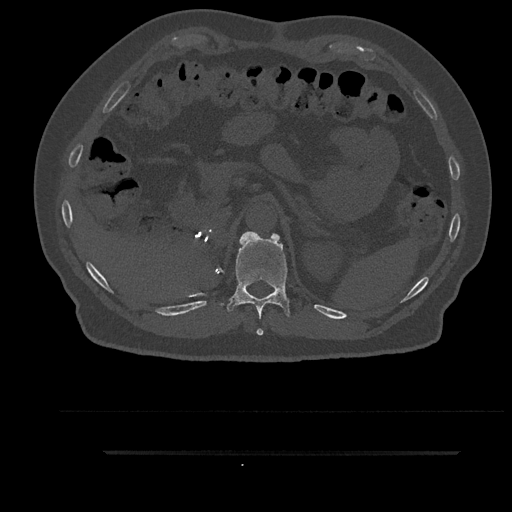
CT including the spine, one axial slice. Reconstruction kernel Br40s/3. 120 kVp. Bone window (W 1800 / L 400 HU). 0.5 mm slice thickness. 512 × 512 image matrix. Male patient, age 63 years. Case-level facts recorded for this patient, not image findings: primary cancer: renal.
Outlined on this slice (semi-automatic segmentation, software-assisted and operator-edited):
- T11 vertebra: box from (x=221, y=231) to (x=296, y=336) px